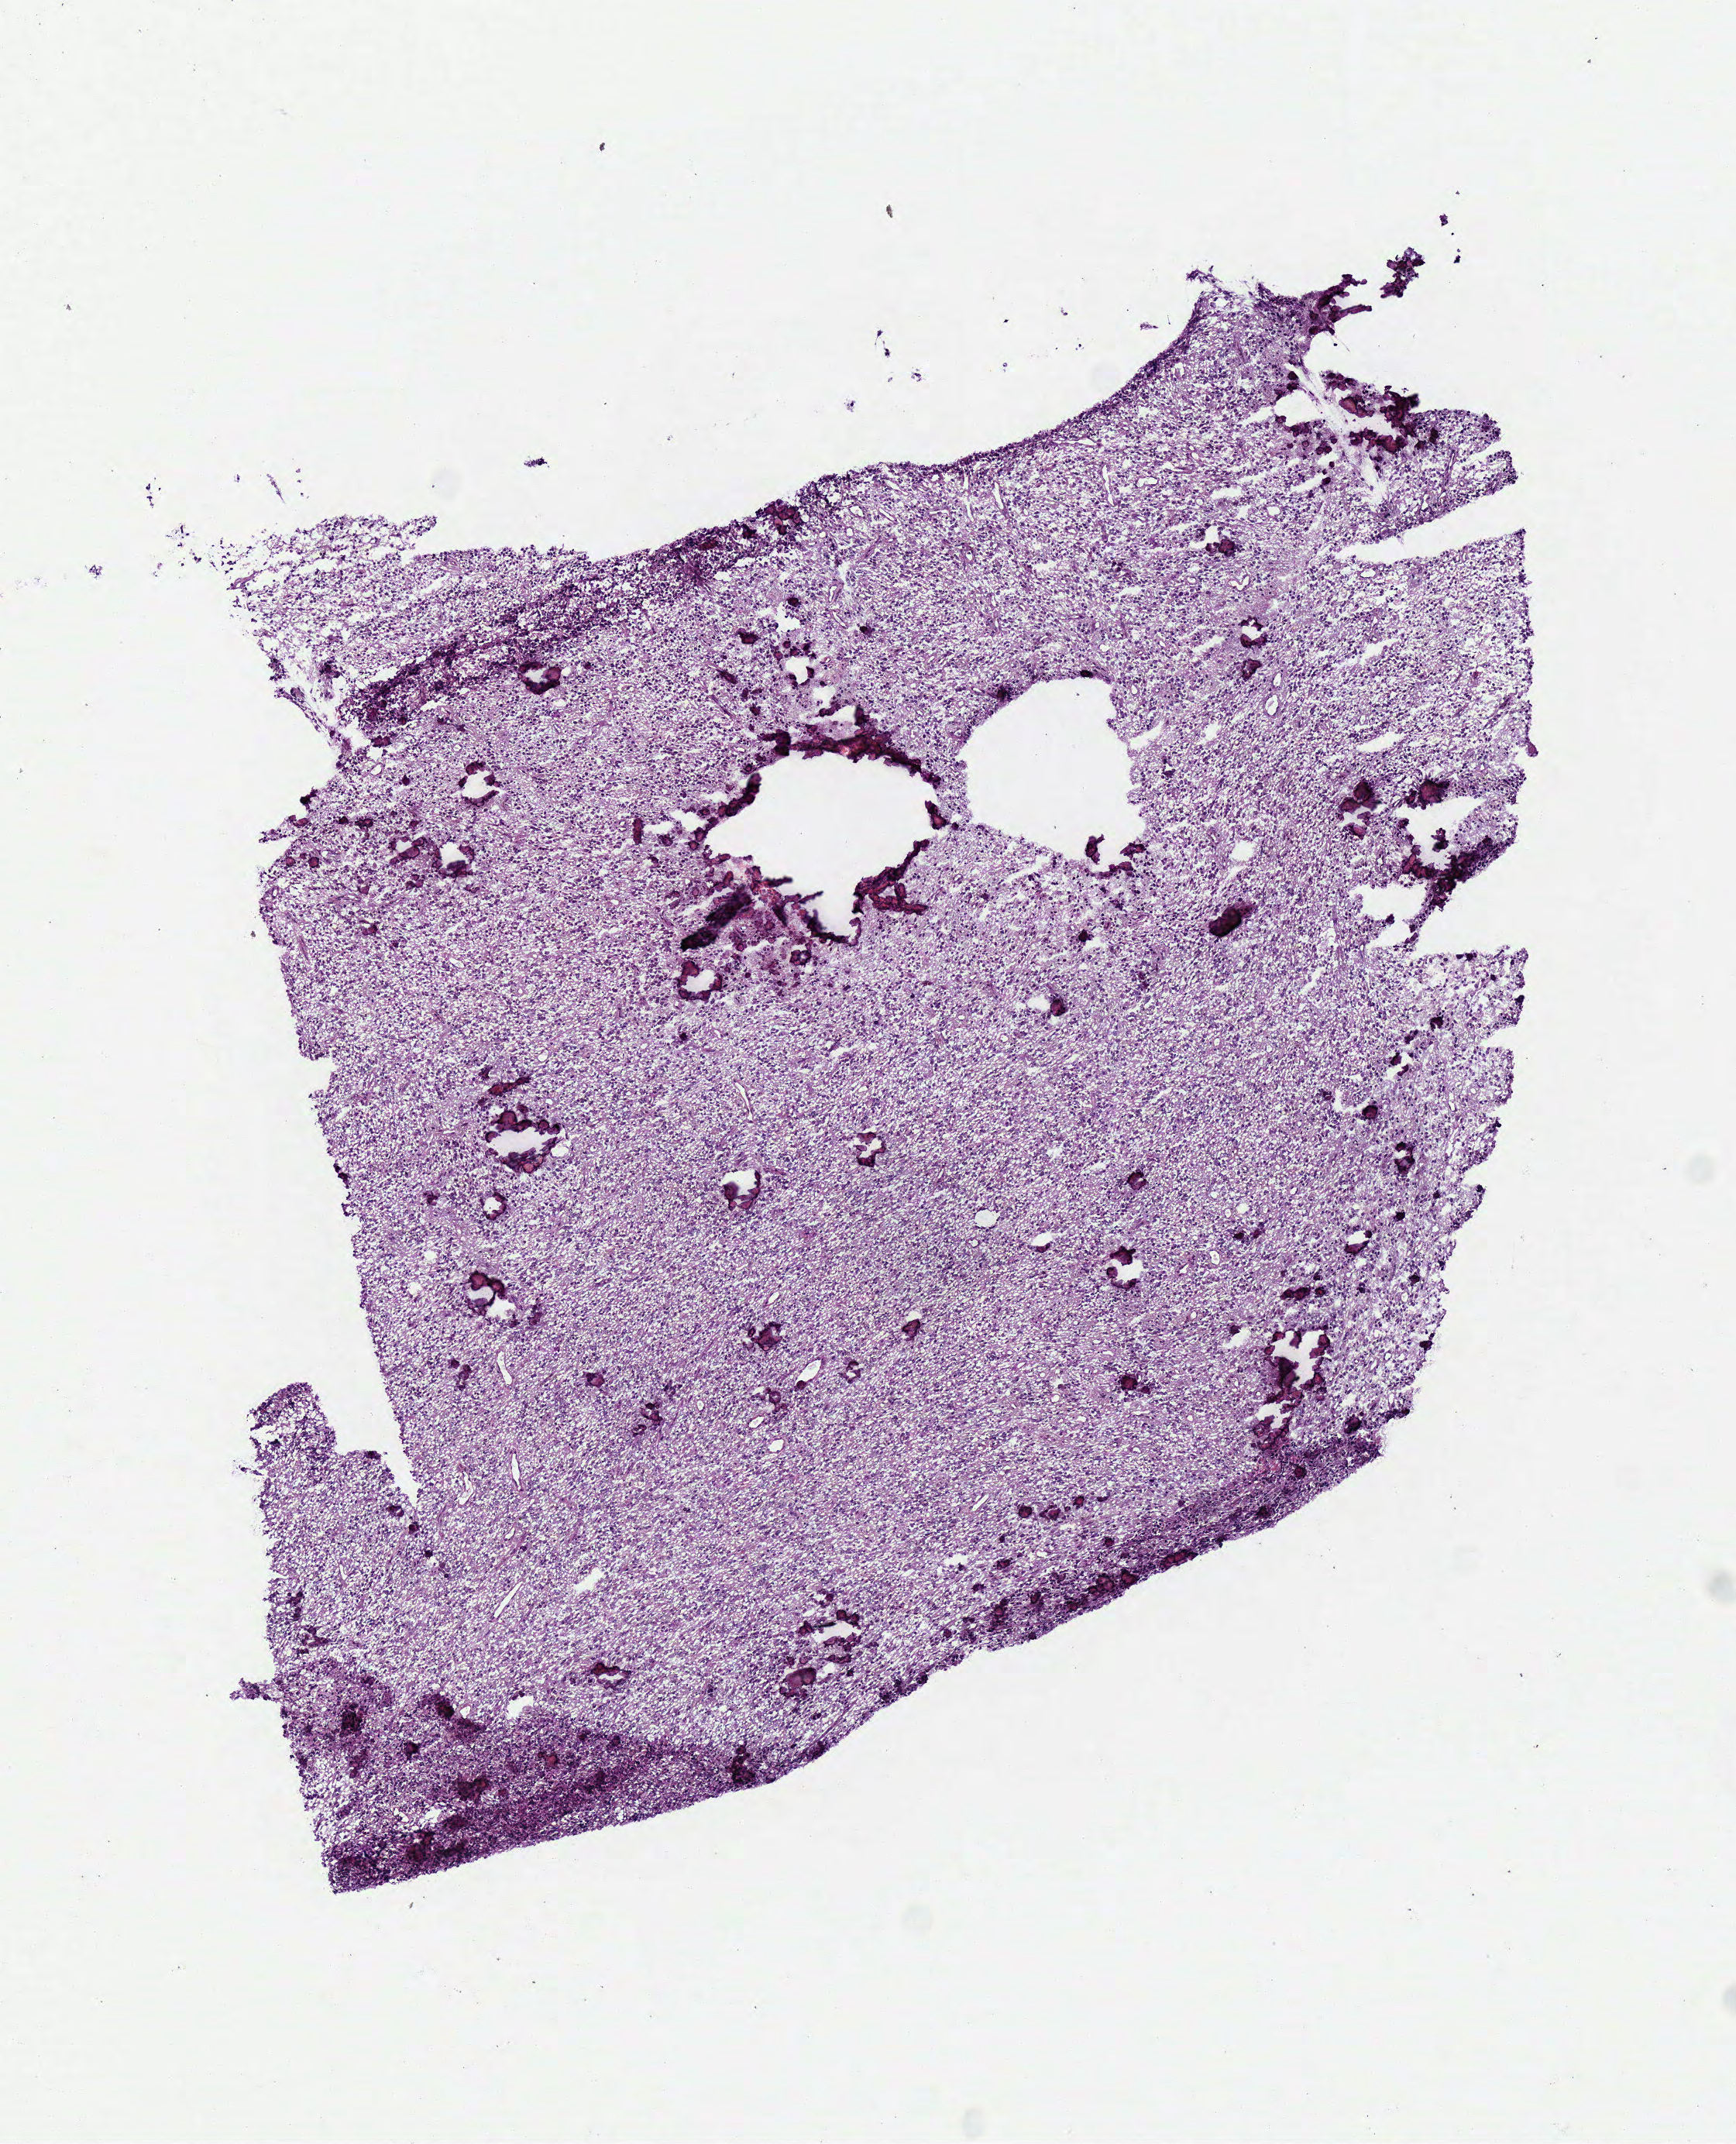
H&E-stained whole-slide image — a low-resolution overview of the entire scanned area, about 4.4 x 5.4 mm (acquisition: 40x scan); frozen section; sample: primary tumour, brain. Female patient; age at initial diagnosis 24 years.
Diagnosis: Oligodendroglioma, anaplastic (cerebrum).